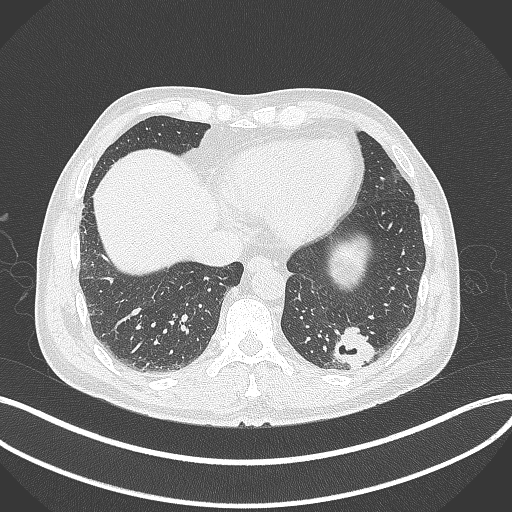
Chest CT, one axial slice; slice 69 of 300 in the series (ordered by position); 120 kVp; lung window (W 1500 / L -600 HU); 1 mm slice thickness; 512 × 512 image matrix. Patient: male, 54 years. From the clinical record (not read from this slice): clinical TNM (as recorded): T1c N0 M1.
Outlined on this slice (bounding box drawn by a radiologist):
- lung tumour (recorded histology: adenocarcinoma): bounding box [x1, y1, x2, y2] px = [331, 323, 376, 374]